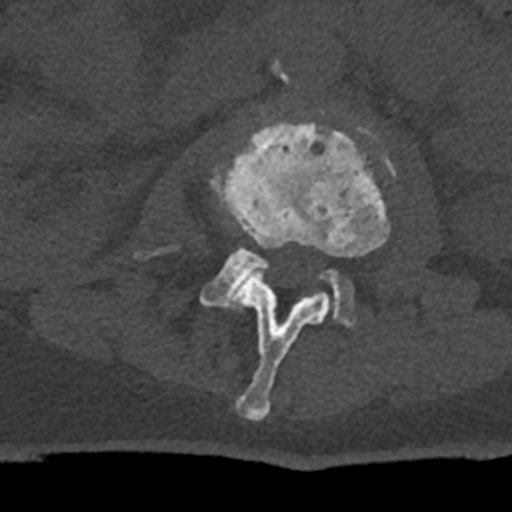
CT including the spine, one axial slice; slice 355 of 797 in the series (ordered by position); reconstruction kernel Br40s/3; bone window (W 1800 / L 400 HU); 512 × 512 image matrix, field of view 160 × 160 mm. Male patient, age 74 years. Case-level facts recorded for this patient, not image findings: primary cancer: renal; vertebrae with lytic lesions (as recorded): T10, L1, L2, L3, L4, L5.
Annotated regions visible in this slice (semi-automatic segmentation, software-assisted and operator-edited):
- L2 vertebra: bounding box (x1, y1, x2, y2) in pixels: (210, 120, 391, 421)
- L3 vertebra: (137, 157, 387, 326)